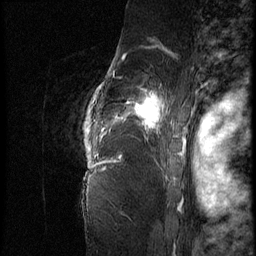
Breast MRI (dynamic contrast-enhanced), one sagittal slice. Slice 55 of 62 in the series (ordered by position). 3 images stored at this slice position (order not interpretable as contrast timing). 1.5 T. TE 4.2 ms, TR 9 ms. 256 × 256 image matrix, field of view 180 × 180 mm. Patient: female, 56 years. Case-level facts recorded for this patient, not image findings: setting: breast cancer imaged before/during neoadjuvant chemotherapy; receptor status: HER2-positive.
Structures marked on this image (semi-automatically segmented with operator editing):
- analysis volume of interest (the breast-tissue region the enhancement analysis was run in; not a lesion): box from (x=84, y=75) to (x=181, y=153) px
- tumour enhancement mask (voxels above the 140 % enhancement threshold inside the analysis volume of interest): (x=85, y=92)–(x=181, y=153)